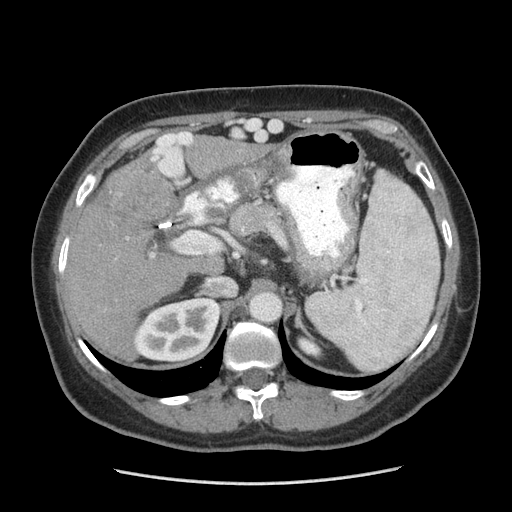
Contrast-enhanced abdominal CT (liver protocol), one axial slice; position 152 of 185 along the scan axis; soft-tissue window (W 400 / L 40 HU); 512 × 512 image matrix, field of view 360 × 360 mm. From the clinical record (not read from this slice): diagnosis: hepatocellular carcinoma (patient treated with transarterial chemoembolisation; whether this scan precedes or follows treatment is not stated here); TNM stage (as recorded): Stage-I; Child-Pugh class: A; tumour differentiation: poorly differentiated; tumour nodularity: uninodular.
Structures marked on this image (semi-automatically segmented with operator editing):
- liver parenchyma outside the tumour (the mass and vessels are separate outlines, so this box may not span the whole liver): box from (x=62, y=132) to (x=252, y=354) px
- mass: (x=105, y=162)–(x=171, y=222)
- liver vessels: (x=66, y=132)–(x=221, y=257)